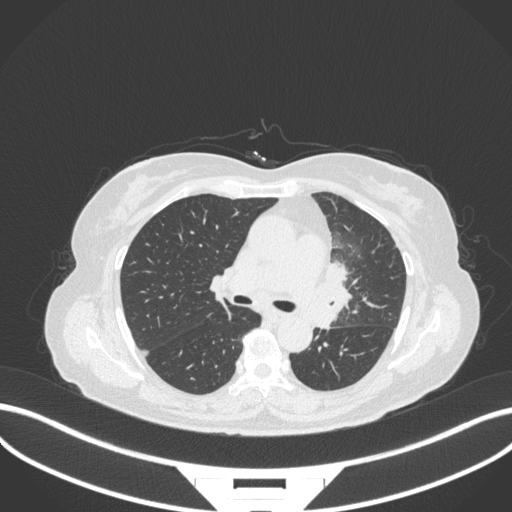
Chest CT, one axial slice. Position 202 of 382 along the scan axis. Reconstruction kernel B31f. 120 kVp. Lung window (W 1500 / L -600 HU). 1 mm slice thickness. 512 × 512 image matrix, field of view 400 × 400 mm. Patient: female, 64 years. From the clinical record (not read from this slice): clinical TNM (as recorded): T2a N2 M0.
Annotated regions visible in this slice (rectangle marked by the reading radiologist):
- lung tumour (recorded histology: adenocarcinoma): bounding box <314,255,357,330> (left, top, right, bottom; pixels)